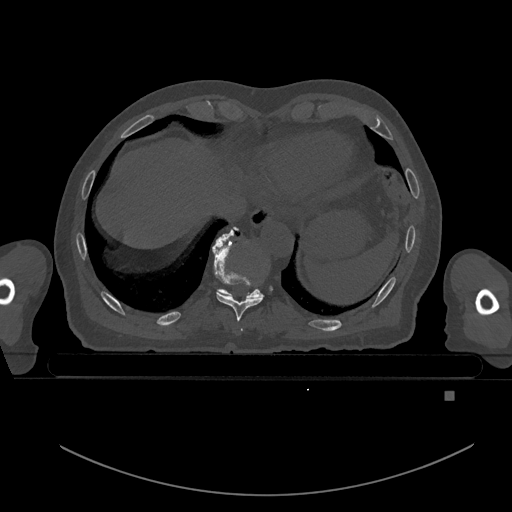
CT including the spine, one axial slice; position 129 of 969 along the scan axis; bone window (W 1800 / L 400 HU); 512 × 512 image matrix. Male patient, age 82 years. From the clinical record (not read from this slice): primary cancer: prostate.
Outlined on this slice (semi-automatic segmentation, software-assisted and operator-edited):
- T10 vertebra: bounding box [x1, y1, x2, y2] px = [219, 227, 261, 297]
- T9 vertebra: [213, 230, 264, 321]